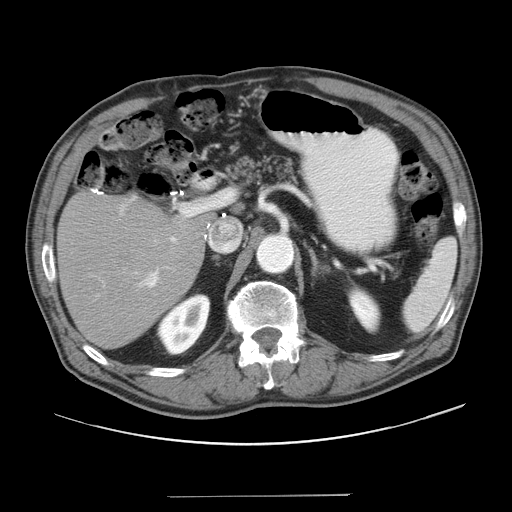
Contrast-enhanced abdominal CT, one axial slice. Slice 23 of 41 in the series (ordered by position). 120 kVp. Intravenous contrast given. Soft-tissue window (W 400 / L 40 HU). 5 mm slice thickness. 512 × 512 image matrix. Male patient, age 75 years. Case-level facts recorded for this patient, not image findings: diagnosis: colorectal cancer liver metastases, imaged before liver resection; multiple liver metastases: no.
Annotated regions visible in this slice (outlined manually by an expert reader):
- liver: bounding box <59,192,208,348> (left, top, right, bottom; pixels)
- planned liver remnant (the part of the liver to remain after resection): <60,192,208,347>
- portal vein (with intrahepatic branches): <119,203,195,288>